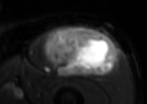
MRI of an extremity soft-tissue mass, one axial slice; slice 51 of 85 in the series (ordered by position); T2-weighted fat-saturated; MR volume resampled by the dataset authors to the PET/CT grid (not the native acquisition matrix); 3.27 mm slice thickness; 147 × 104 image matrix, field of view 144 × 102 mm. Male patient. From the clinical record (not read from this slice): histological type: extraskeletal osteosarcoma; grade: high; site of the primary tumour: thigh.
Structures marked on this image (expert contour drawn on MRI and transferred to this co-registered scan by the dataset authors):
- gross tumour volume (mass): bounding box <42,26,118,77> (left, top, right, bottom; pixels)